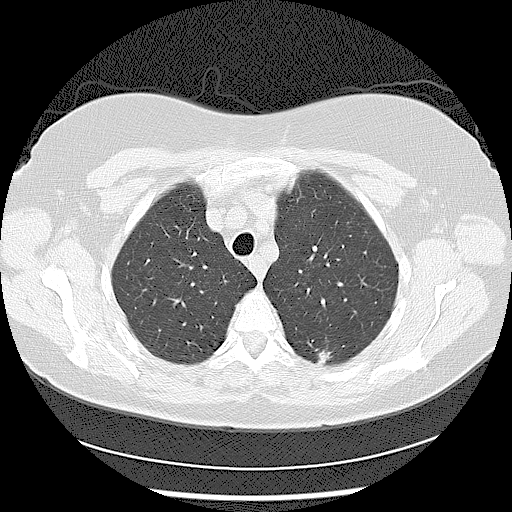
Axial slice from a low-dose chest CT screening exam, first (baseline) screen, lung window (W 1500 / L -600 HU), lung (sharp) reconstruction kernel (LUNG), slice 23 of 116 in the series. Female, age 56 years at enrolment. Current smoker at enrolment.
Lesion marked by an expert reader, bounding box [x1, y1, x2, y2] px = [297, 330, 347, 376]. The screening reader recorded 2 non-calcified nodules or masses ≥4 mm on this exam; which of them this box marks is not recorded. Participant outcome: lung cancer diagnosed 638 days after this screen (after the second annual screen) — adenocarcinoma, NOS, left lower lobe, moderately differentiated (G2), stage IIA (AJCC 6th edition), 15 mm at pathology.